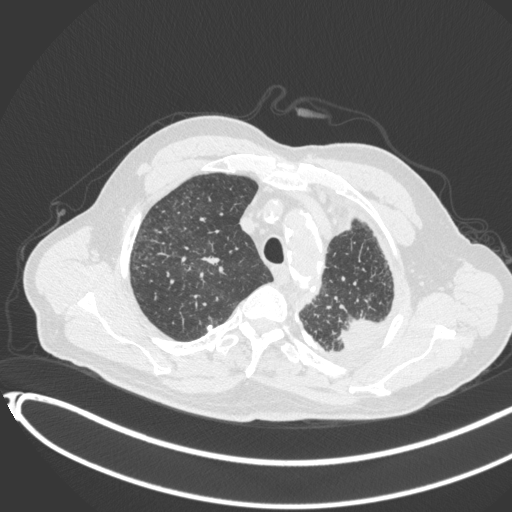
Chest CT, one axial slice; position 349 of 451 along the scan axis; reconstruction kernel B31f; 120 kVp; lung window (W 1500 / L -600 HU); 512 × 512 image matrix, field of view 400 × 400 mm. Male patient, age 78 years. Case-level facts recorded for this patient, not image findings: clinical TNM (as recorded): T1c N0 M1.
Outlined on this slice (rectangle marked by the reading radiologist):
- lung tumour (recorded histology: adenocarcinoma): box from (x=333, y=311) to (x=386, y=359) px